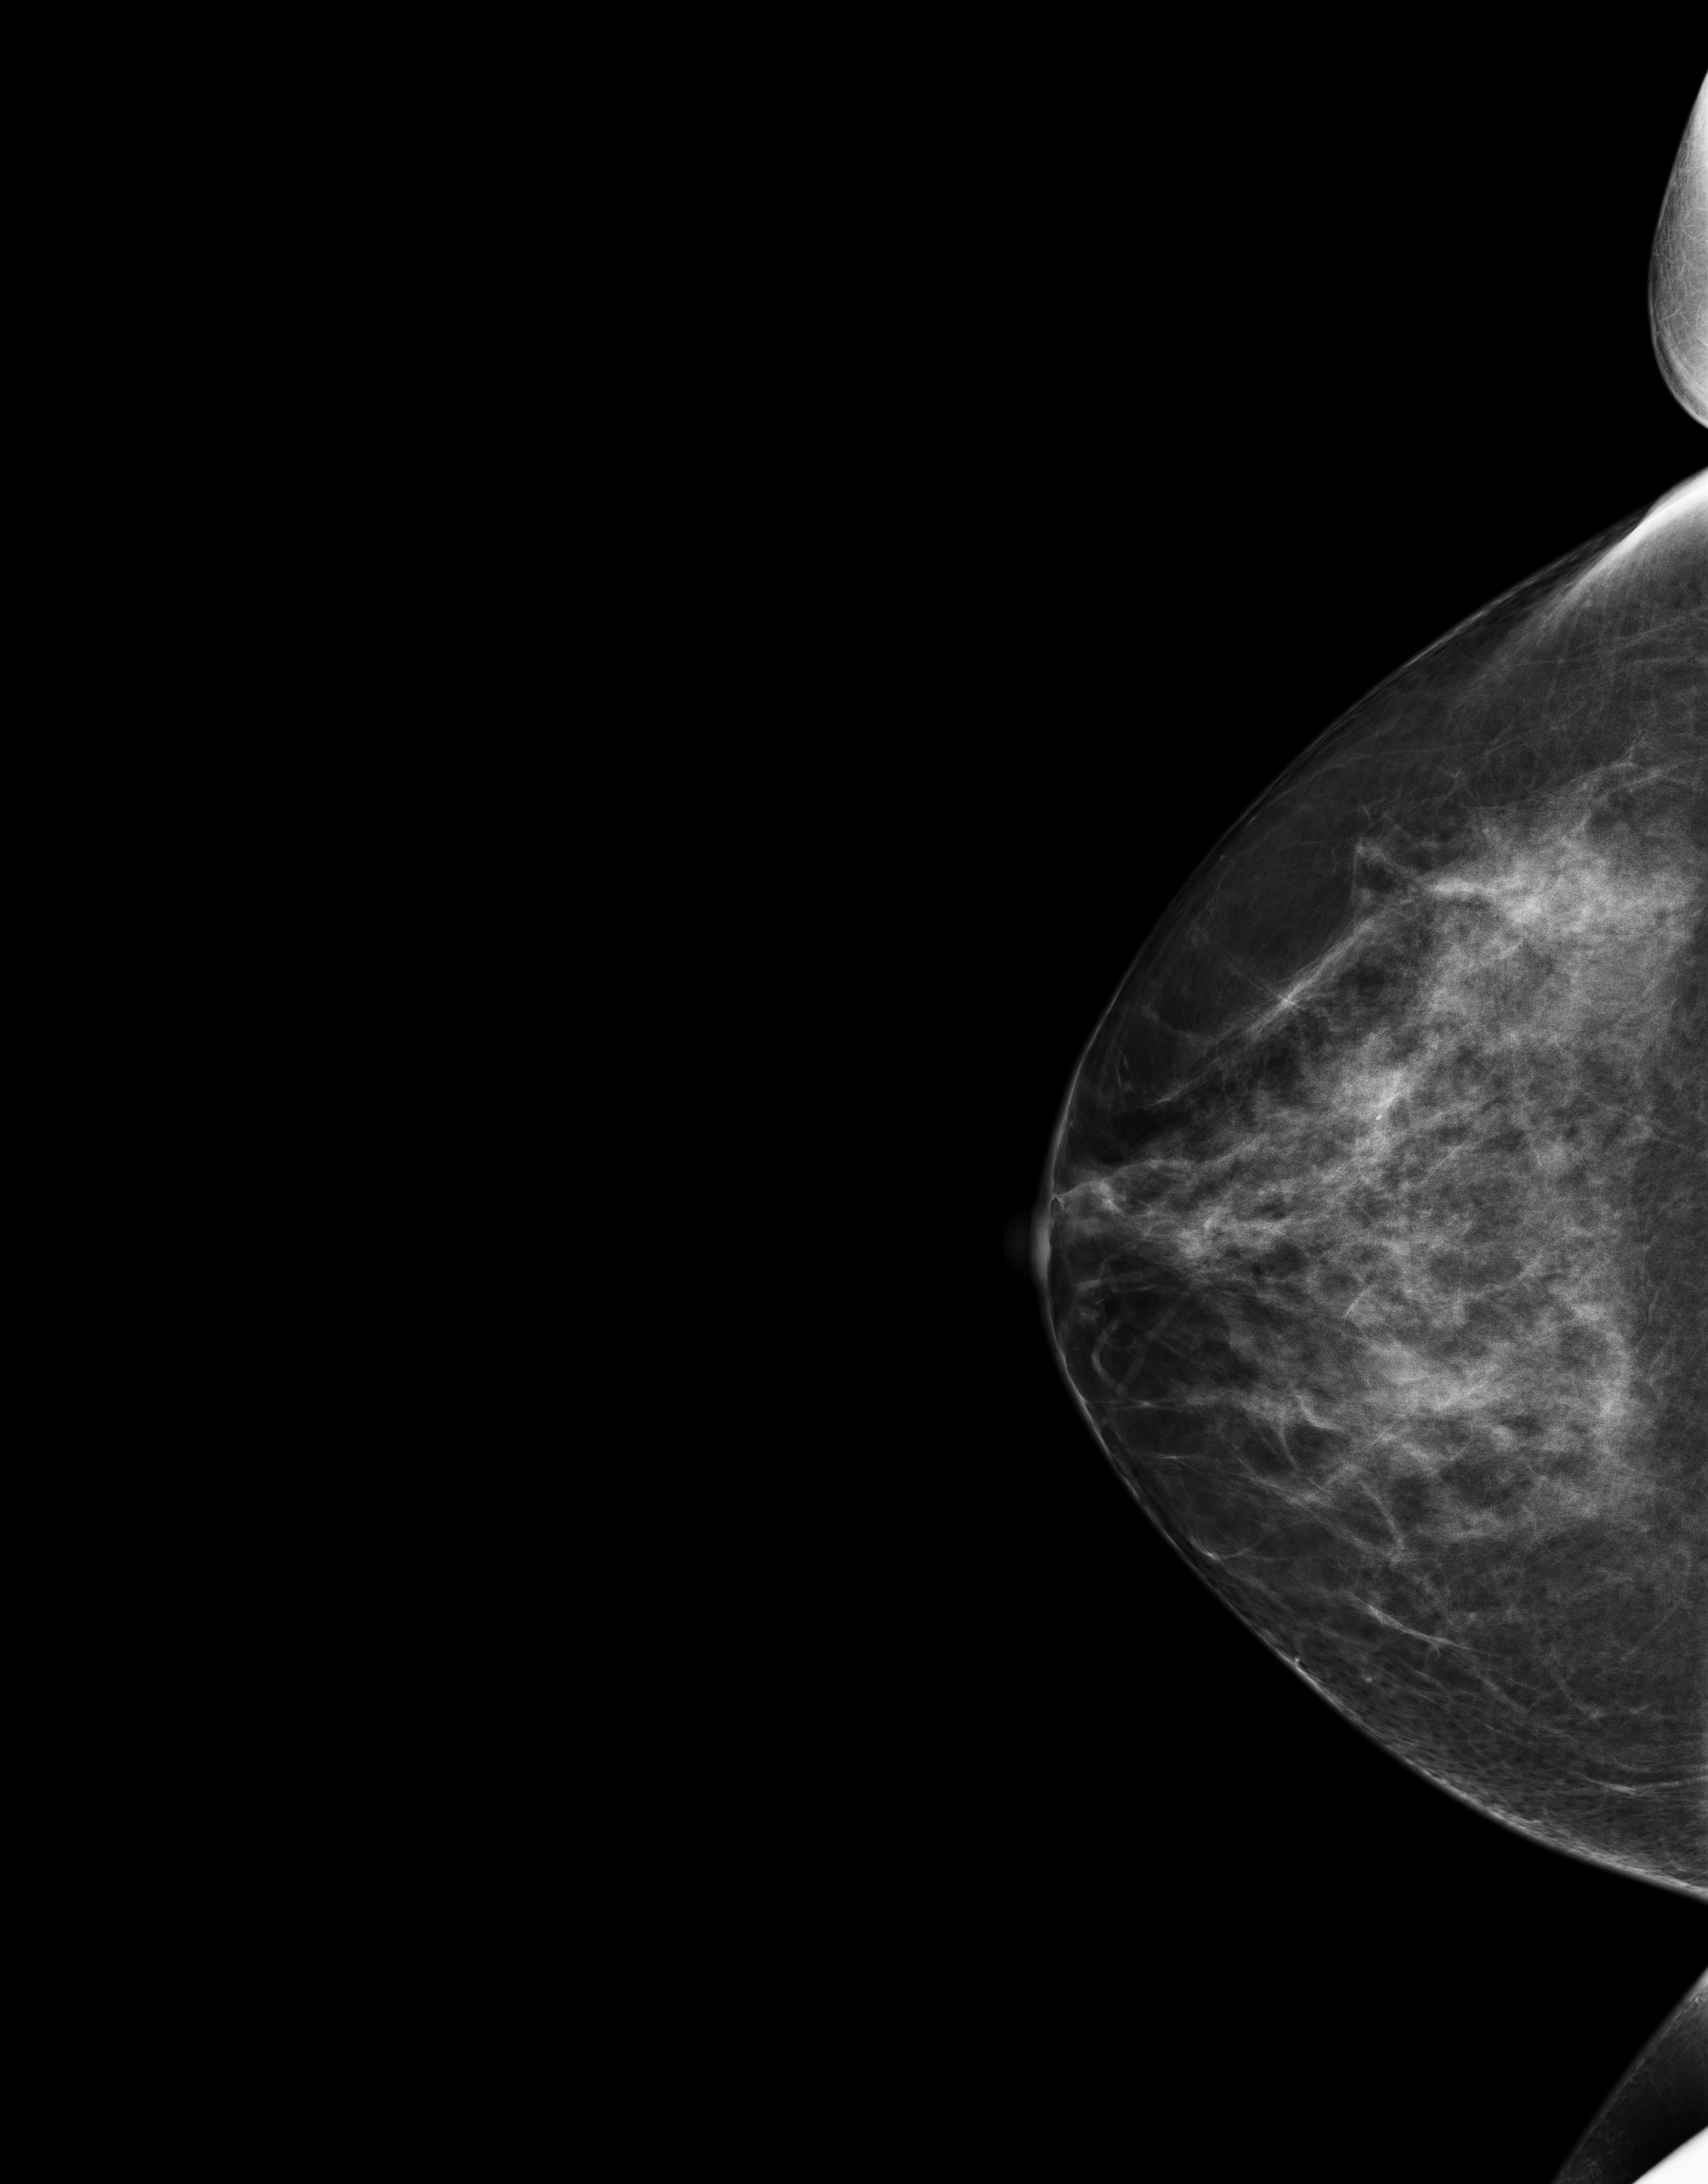
Screening examination. Patient aged 46 years (female).
Image type: full-field digital mammogram. Breast: right. Projection: CC view.